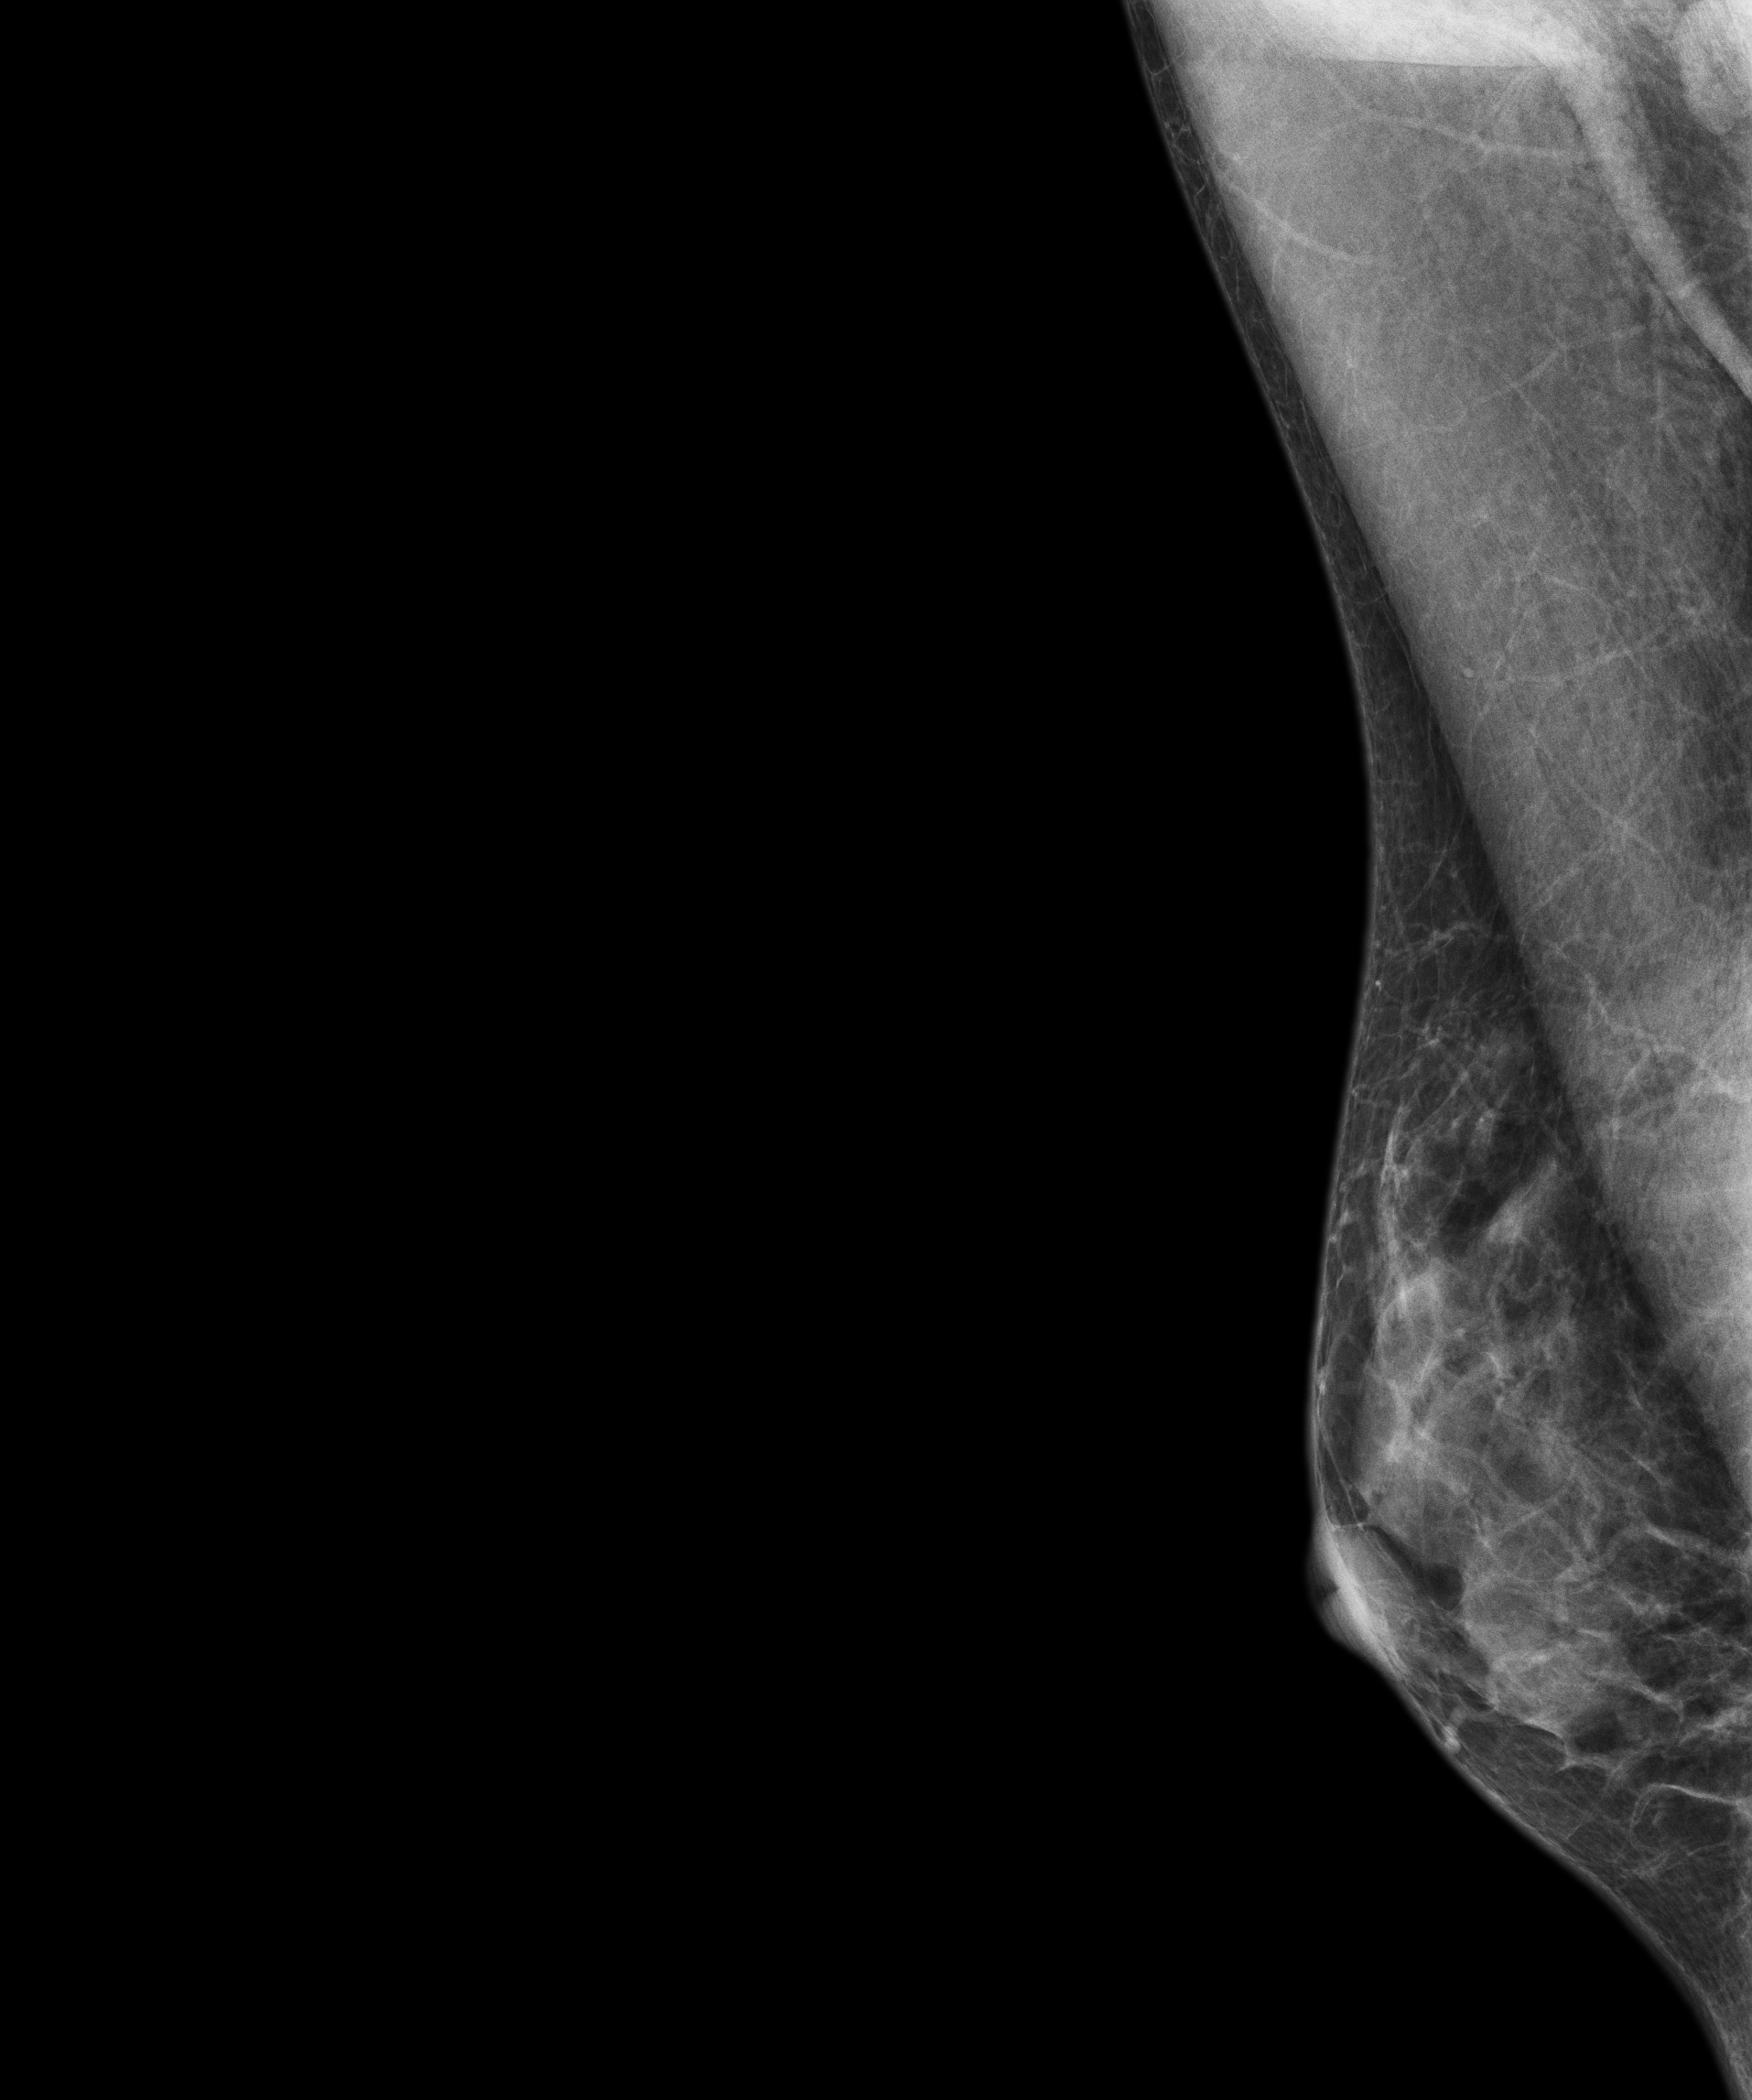
Annual screening mammography examination, system: Senographe Essential ADS_56.21.3. Female patient, age 56 years.
Image type: full-field digital mammogram. Breast: right. Projection: medio-lateral oblique projection.